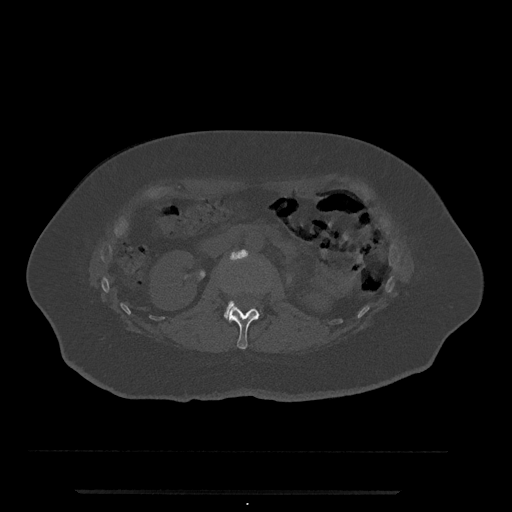
CT including the spine, one axial slice; slice 76 of 797 in the series (ordered by position); reconstruction kernel Br40s/3; 120 kVp; bone window (W 1800 / L 400 HU); 0.5 mm slice thickness; 512 × 512 image matrix, field of view 440 × 440 mm. Patient: female, 51 years. Case-level facts recorded for this patient, not image findings: primary cancer: neuro.
Structures marked on this image (semi-automatically segmented with operator editing):
- L1 vertebra: bounding box (x1, y1, x2, y2) in pixels: (225, 307, 260, 349)
- L2 vertebra: (225, 301, 263, 314)